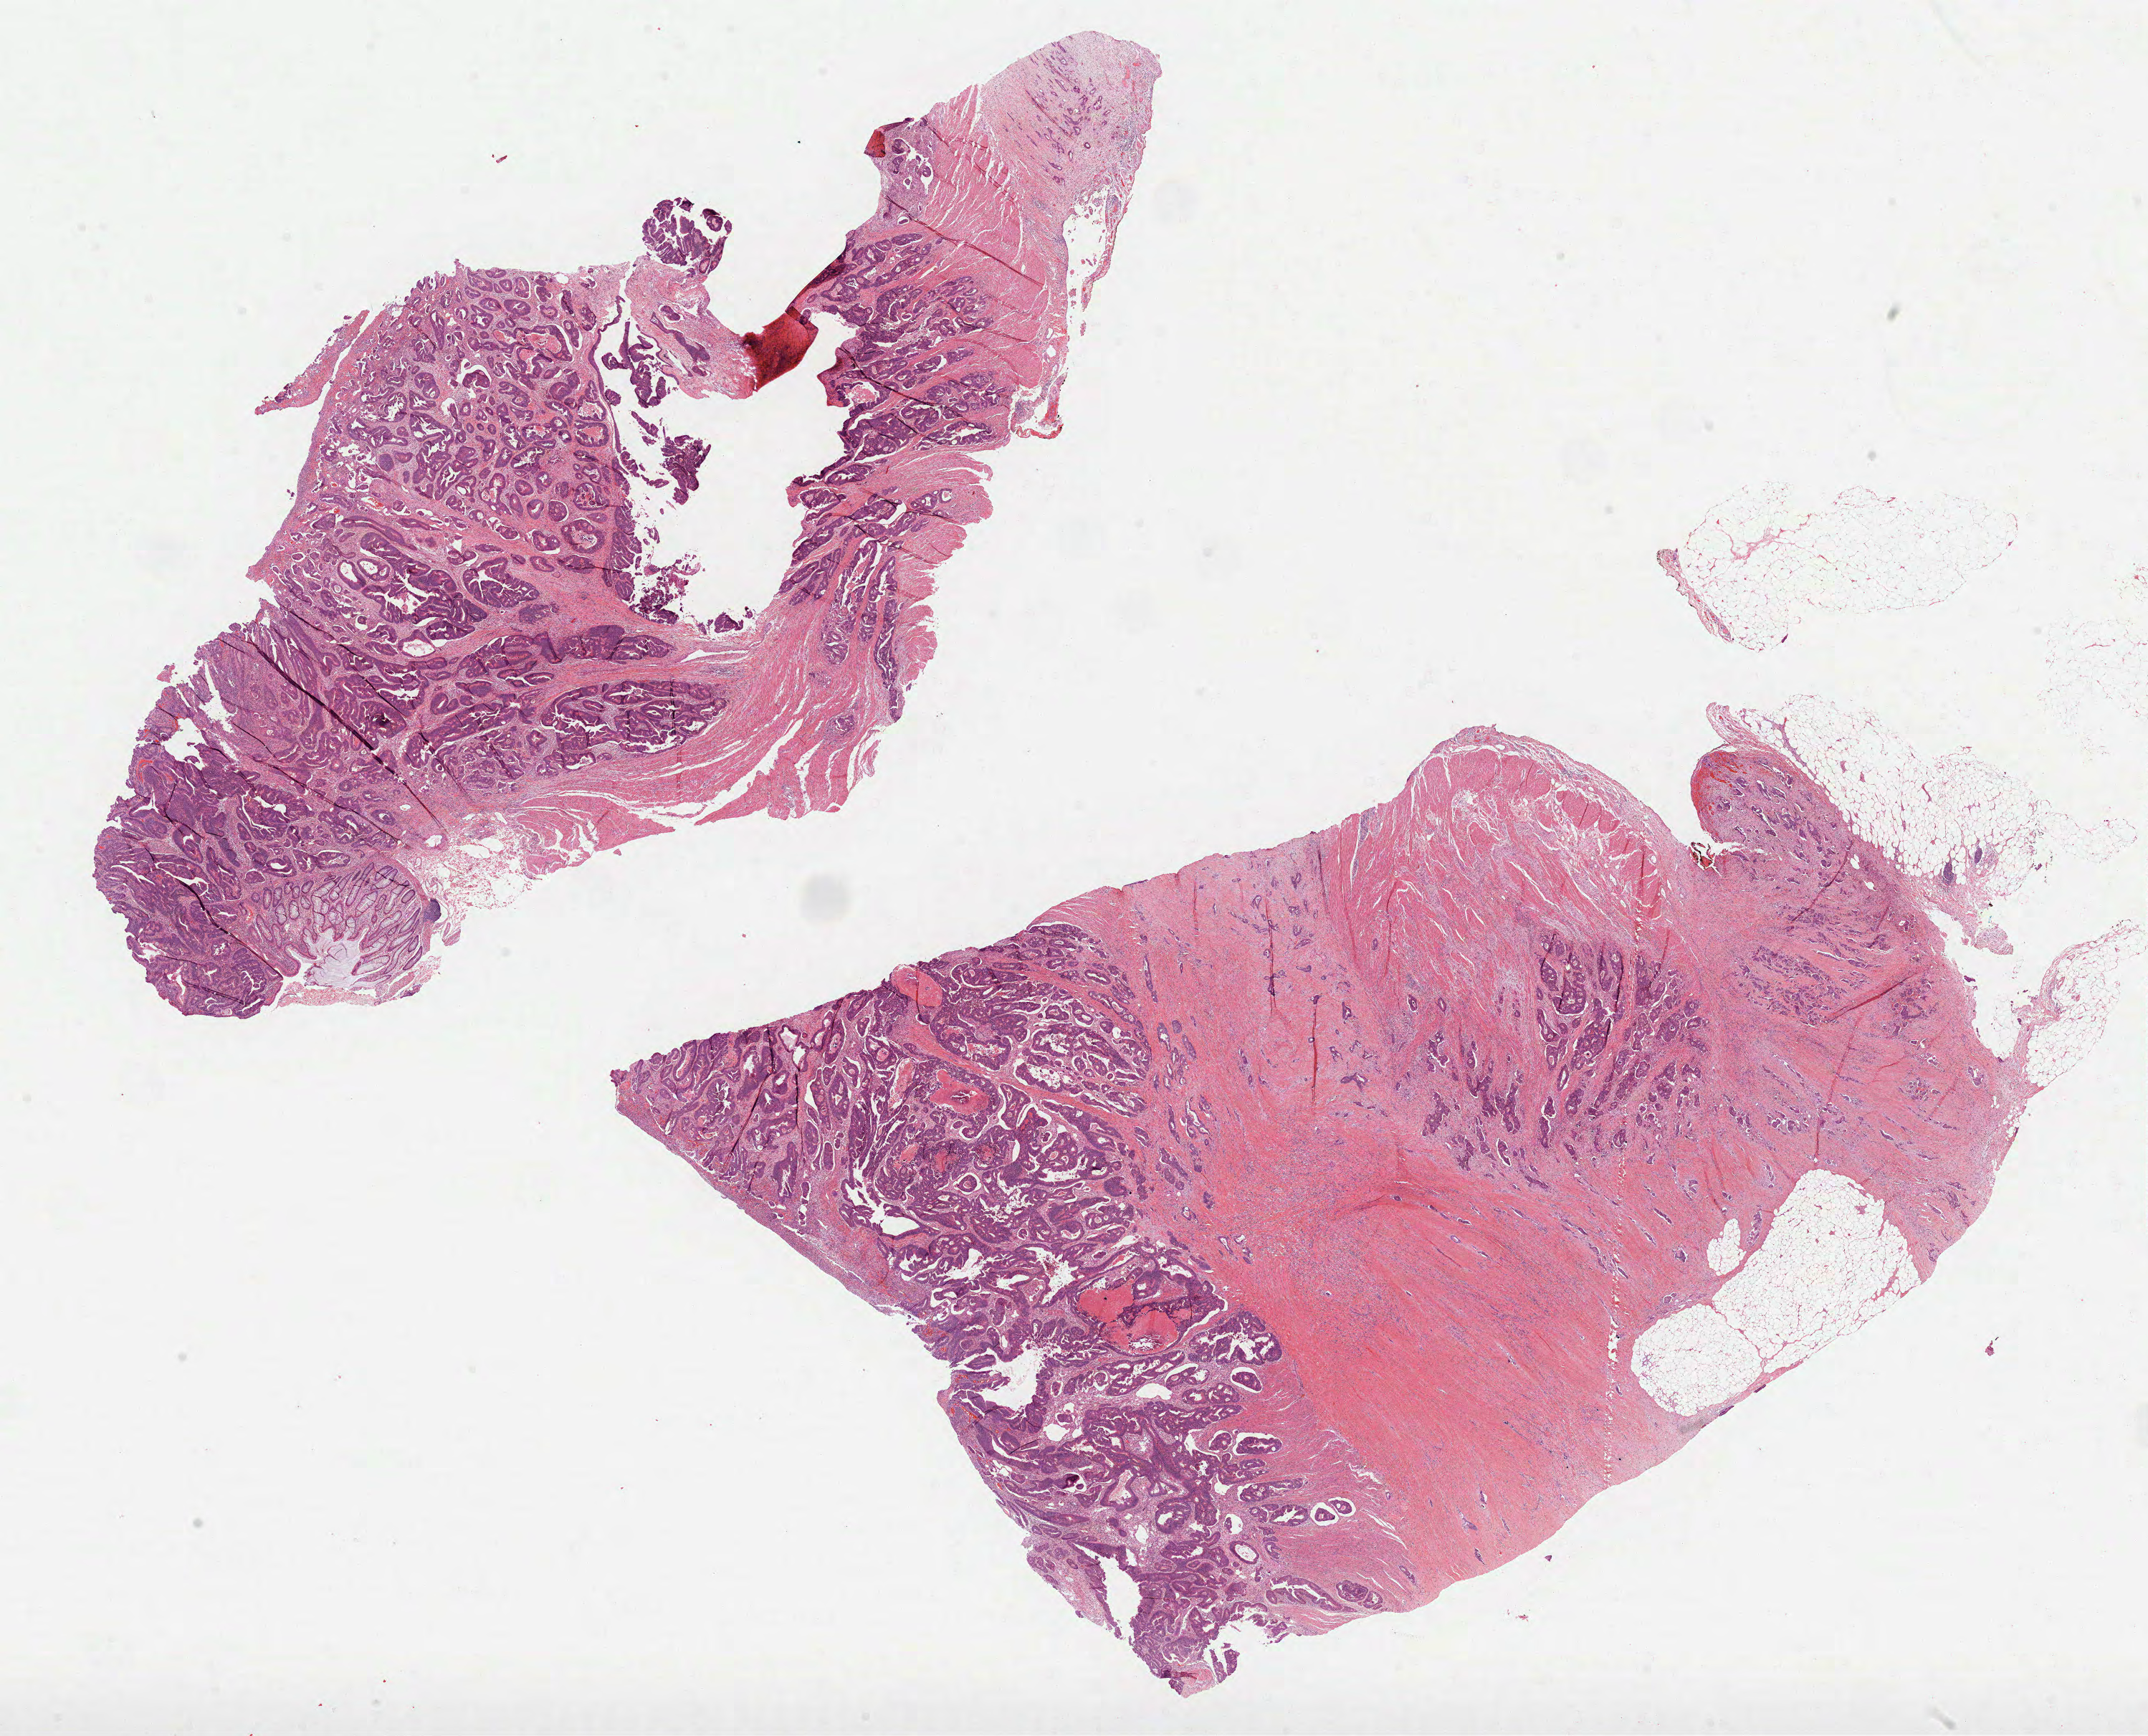
Digitized Hematoxylin and eosin (H&E) stained tissue section (whole slide) — whole scanned area (about 24.2 x 19.5 mm) shown as a low-resolution overview, FFPE section, sample: primary tumour, colon. Female, age 54 years at initial diagnosis.
Pathologic diagnosis: Adenocarcinoma, NOS. AJCC pathologic stage: IV.